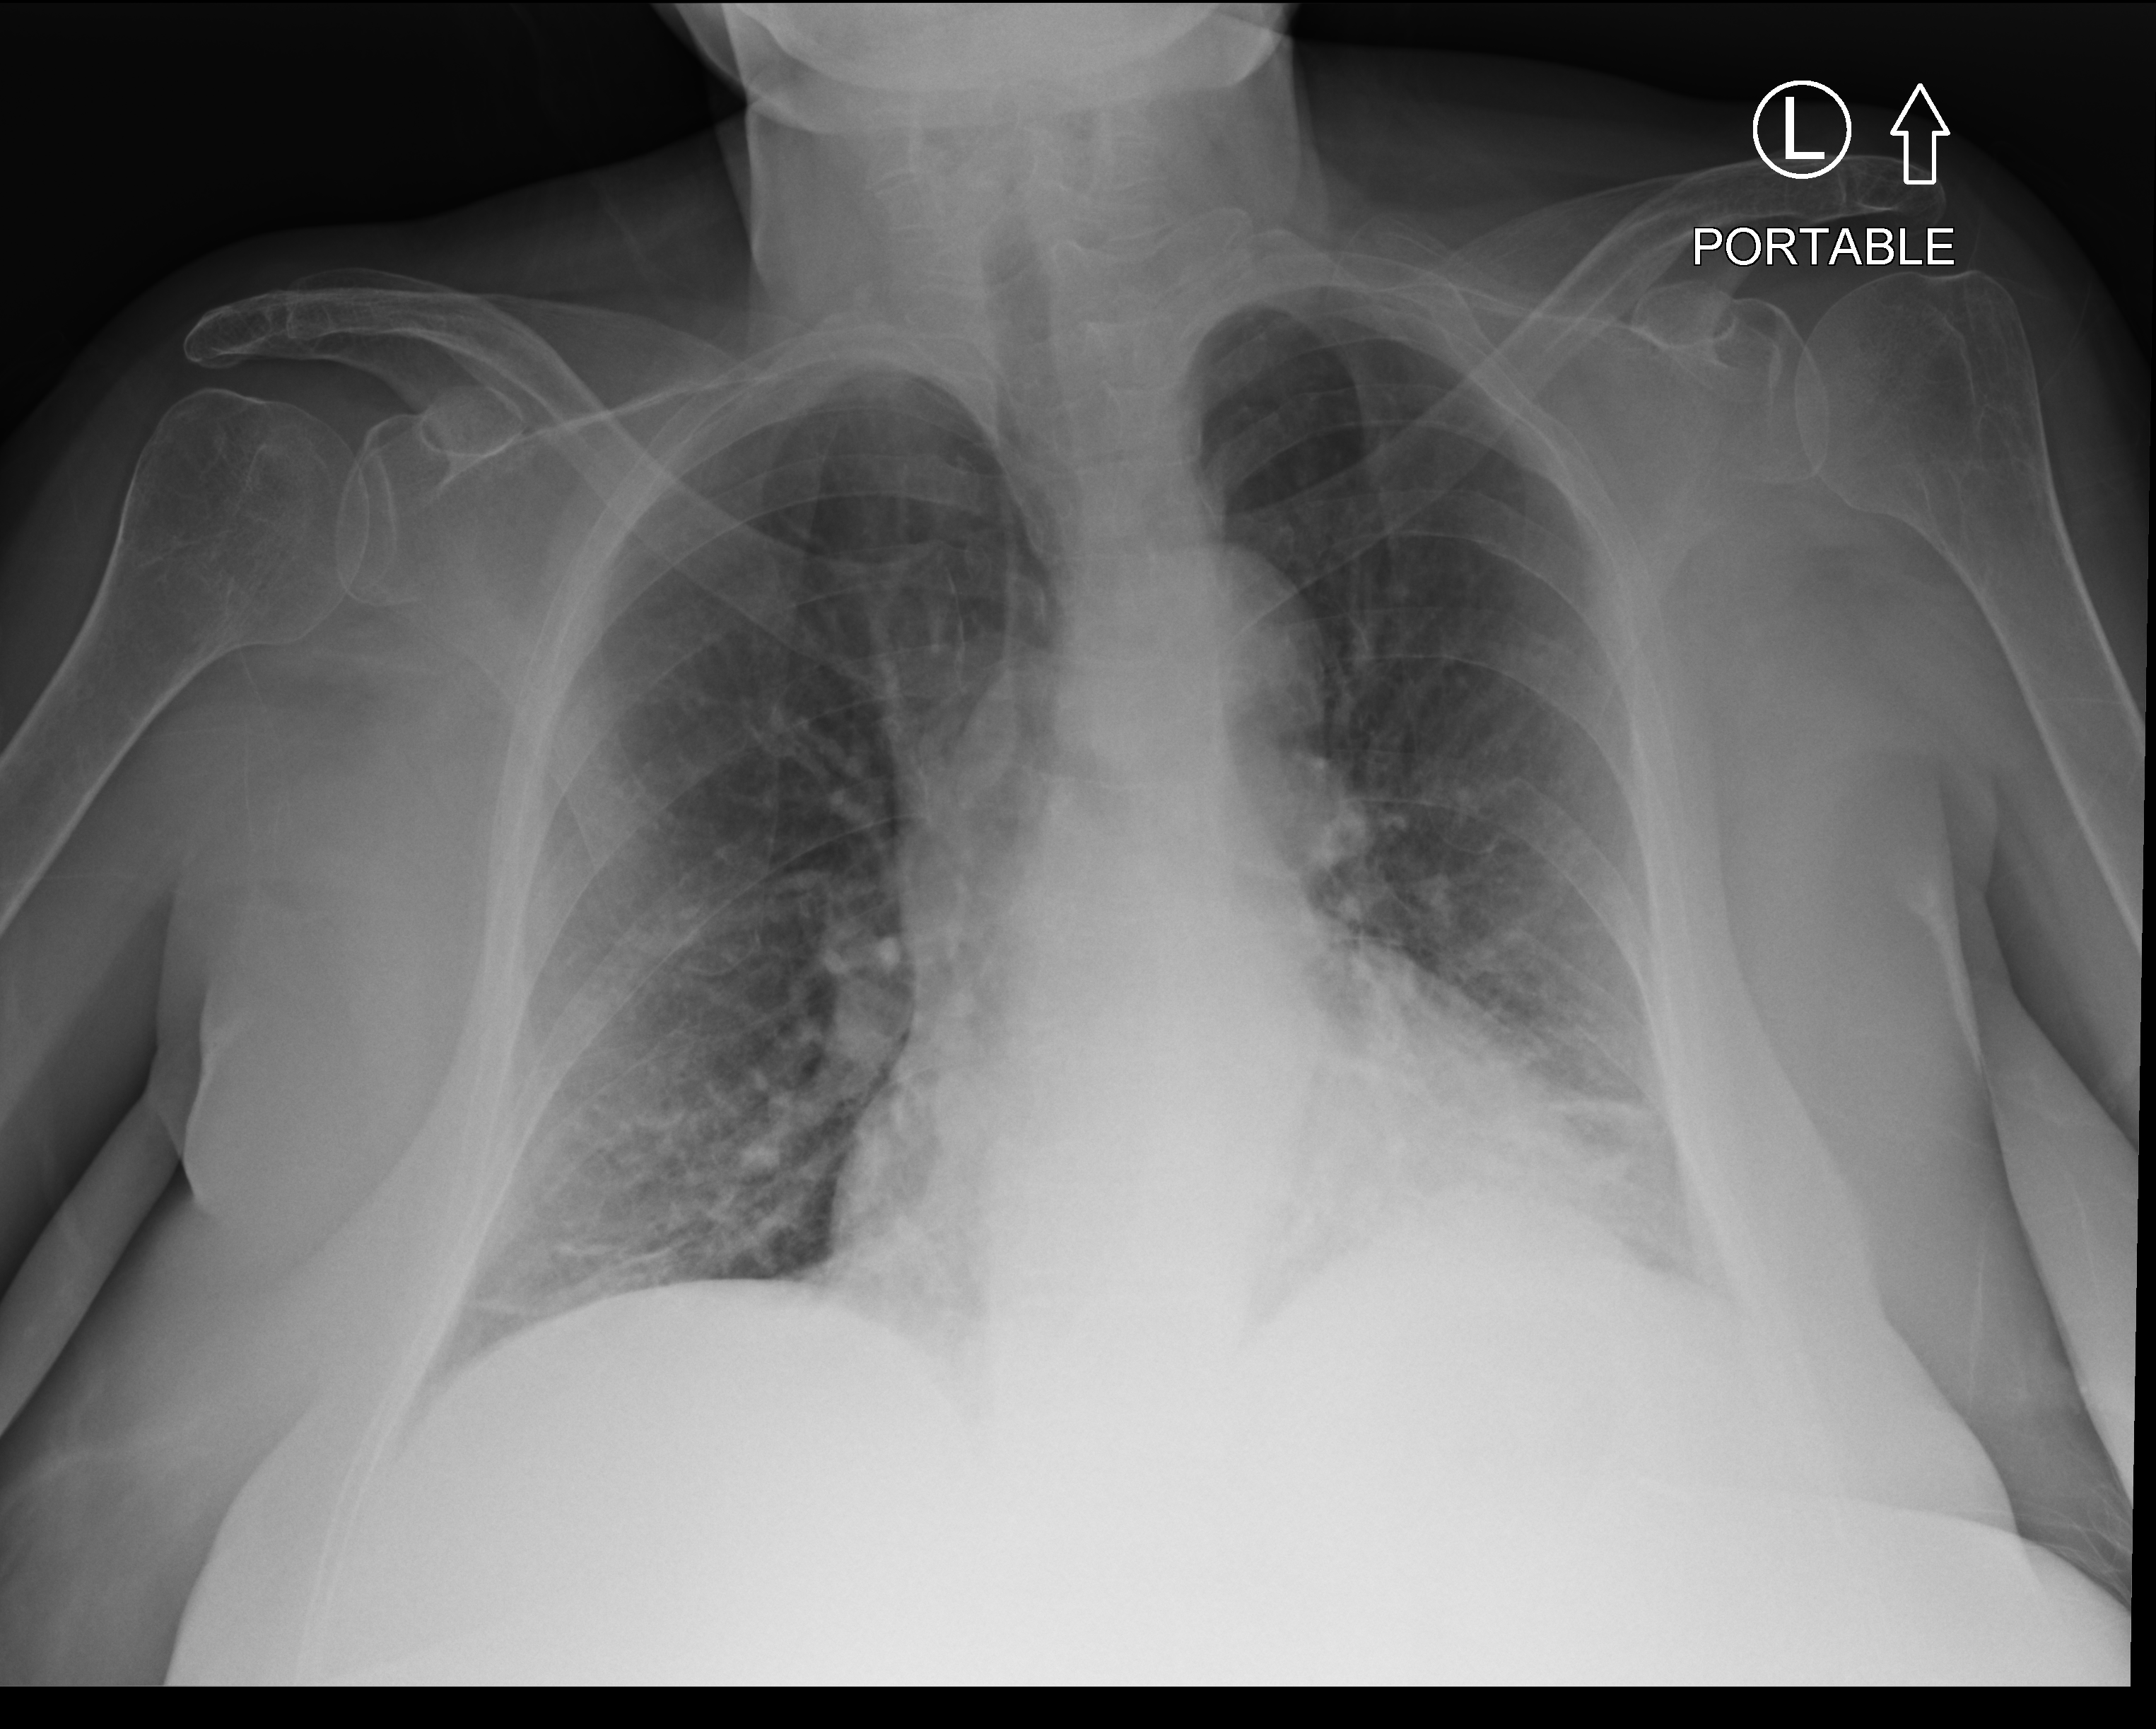
Portable chest radiograph, anteroposterior (AP) projection. Patient hospitalised with COVID-19; female, aged 60–74 years.
From the hospital-stay record, not from the radiograph (when in the stay this image was taken is not recorded): length of hospital stay: 1 day; mechanically ventilated during this hospital stay: no.